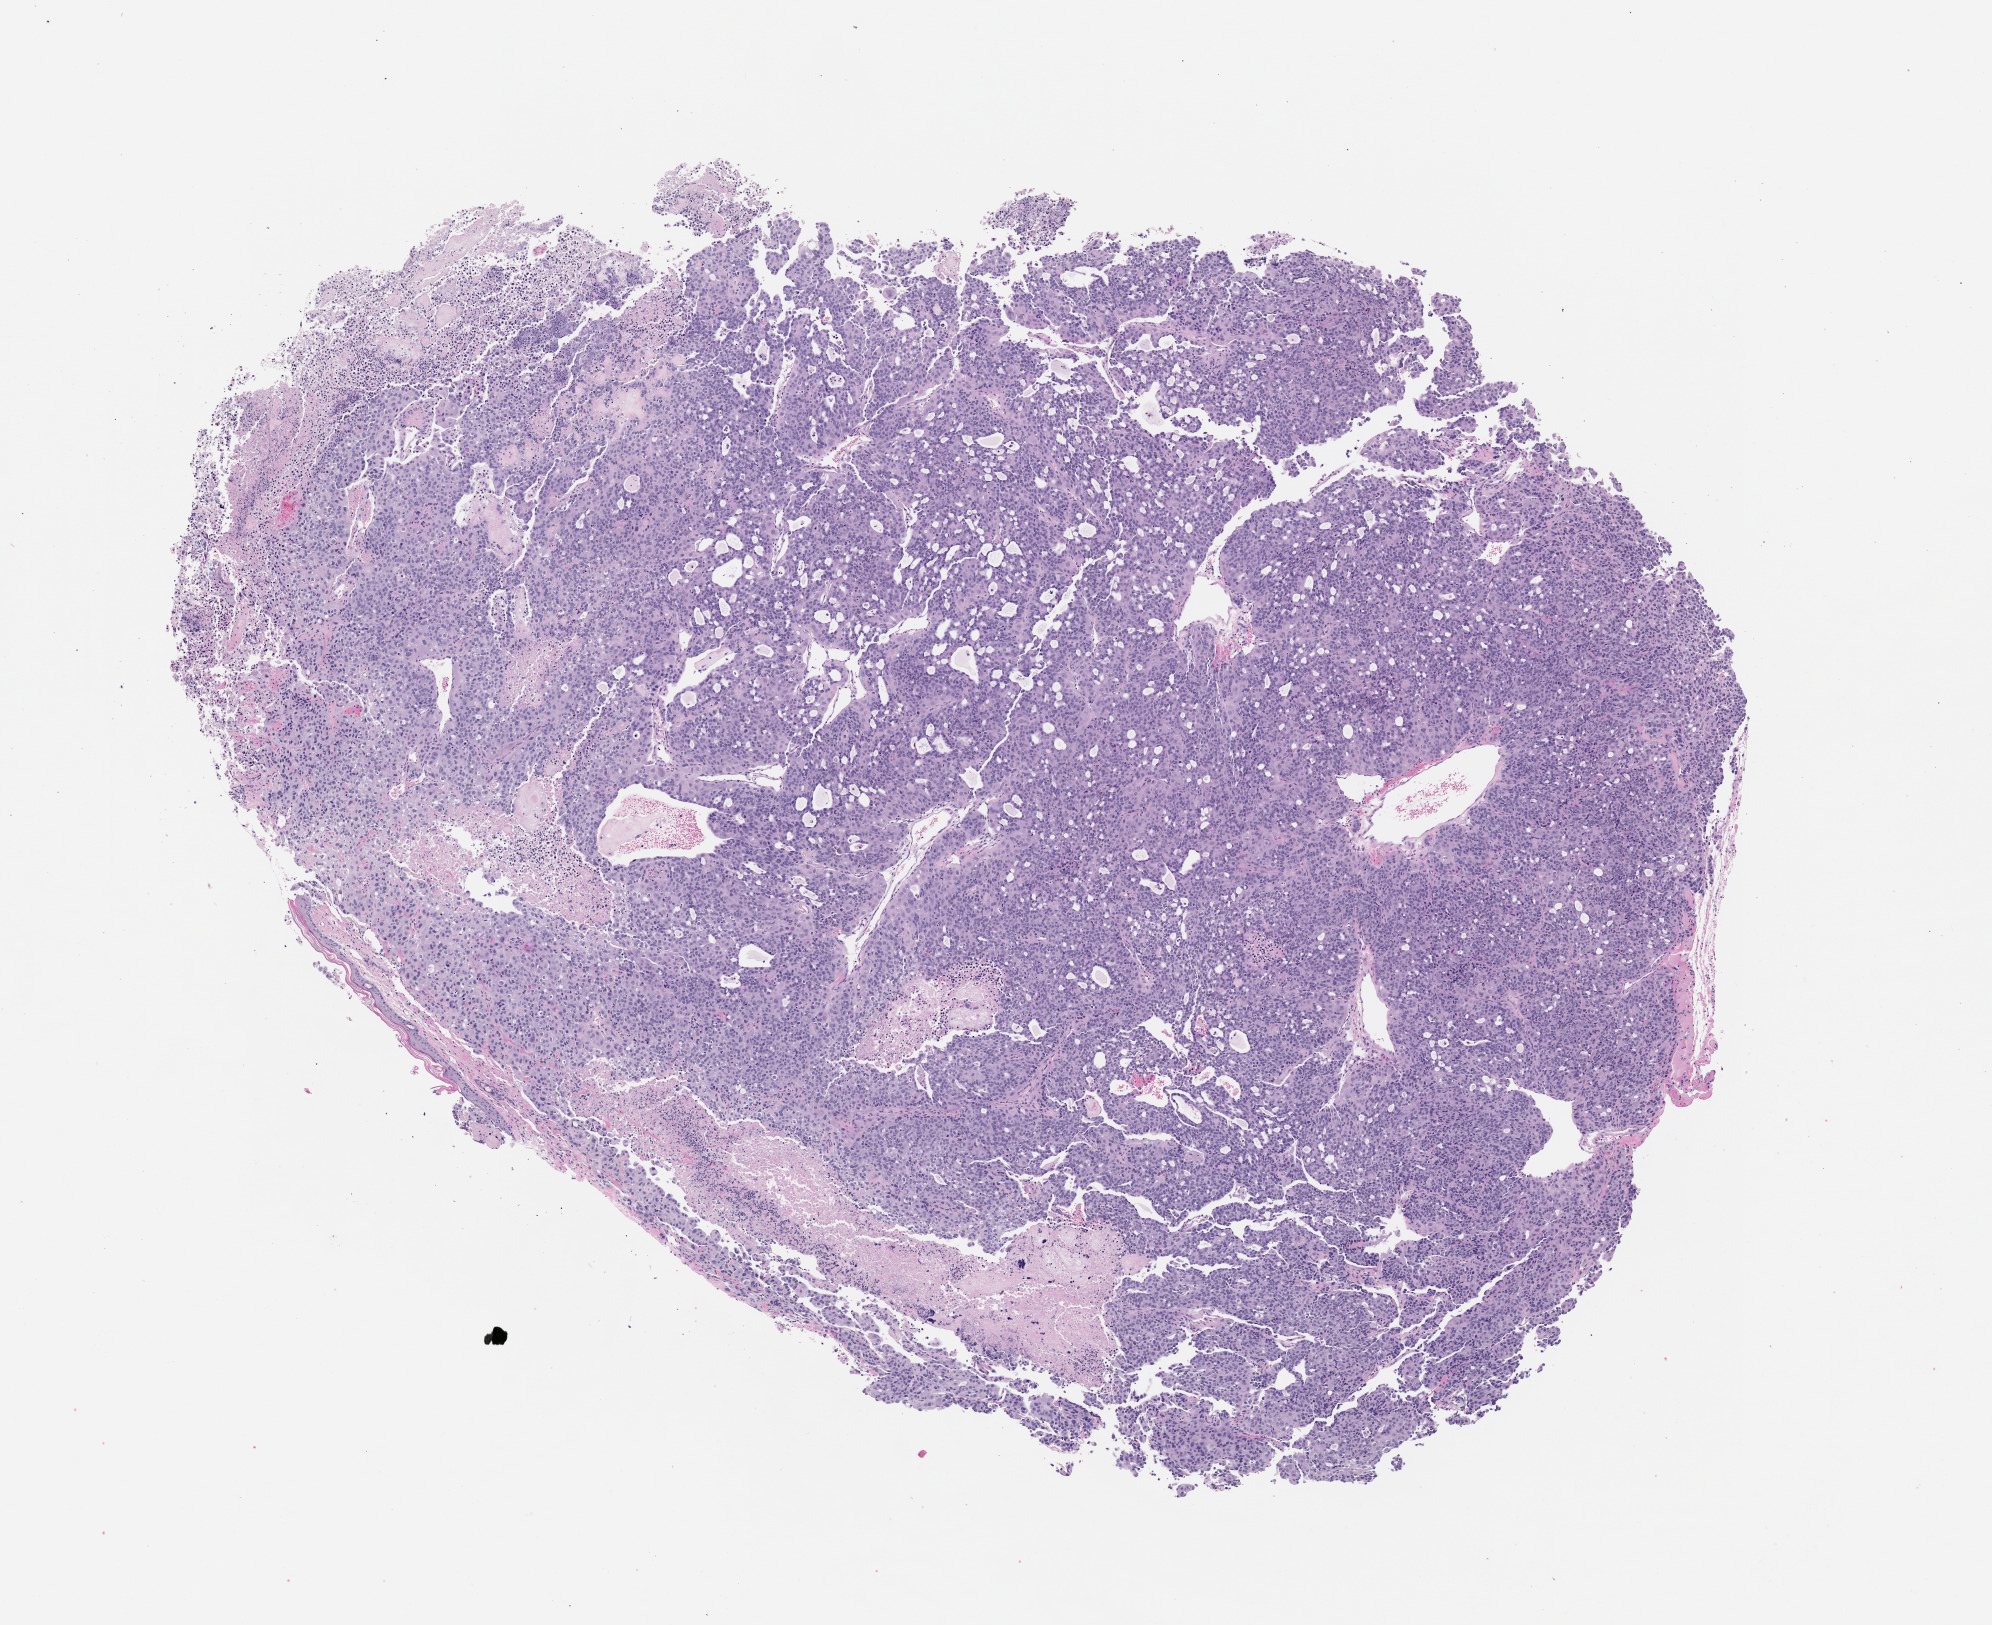
Haematoxylin and eosin whole-slide image of a patient-derived xenograft (PDX) tumor grown in a mouse, passage 3 — shown as a low-resolution overview of the whole scanned area (about 8.0 x 6.5 mm). FFPE section. Tumor site category: bladder.
Originating patient diagnosis: Urothelial Carcinoma.